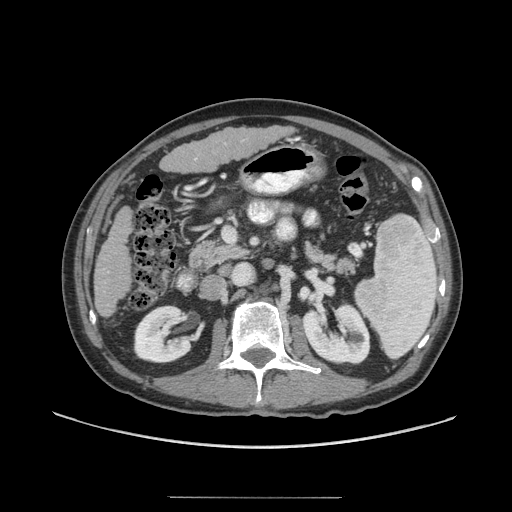
Contrast-enhanced abdominal CT (liver protocol), one axial slice. Position 18 of 71 along the scan axis. Soft-tissue window (W 400 / L 40 HU). 2.5 mm slice thickness. 512 × 512 image matrix, field of view 400 × 400 mm. From the clinical record (not read from this slice): diagnosis: hepatocellular carcinoma (patient treated with transarterial chemoembolisation; whether this scan precedes or follows treatment is not stated here); TNM stage (as recorded): Stage-I; Child-Pugh class: A; tumour differentiation: well differentiated; tumour nodularity: uninodular.
Outlined on this slice (semi-automatically segmented with operator editing):
- liver parenchyma outside the tumour (the mass and vessels are separate outlines, so this box may not span the whole liver): bounding box <94,125,293,318> (left, top, right, bottom; pixels)